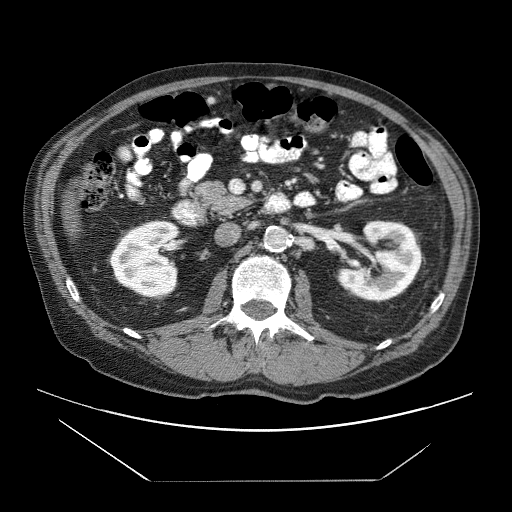
Contrast-enhanced abdominal CT (liver protocol), one axial slice; position 9 of 83 along the scan axis; reconstruction kernel STANDARD; 120 kVp; soft-tissue window (W 400 / L 40 HU); 2.5 mm slice thickness; 512 × 512 image matrix, field of view 420 × 420 mm. Case-level facts recorded for this patient, not image findings: diagnosis: hepatocellular carcinoma (patient treated with transarterial chemoembolisation; whether this scan precedes or follows treatment is not stated here); TNM stage (as recorded): Stage-IVB; Child-Pugh class: B; tumour differentiation: poorly differentiated; tumour nodularity: uninodular.
Annotated regions visible in this slice (semi-automatic segmentation, software-assisted and operator-edited):
- liver parenchyma outside the tumour (the mass and vessels are separate outlines, so this box may not span the whole liver): bounding box (x1, y1, x2, y2) in pixels: (62, 201, 79, 242)